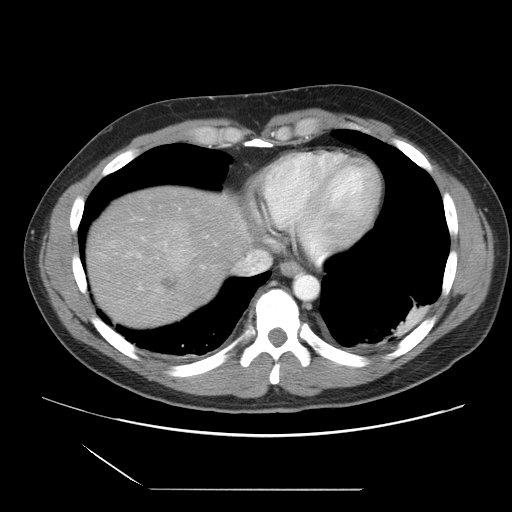
Contrast-enhanced abdominal CT, one axial slice; slice 30 of 39 in the series (ordered by position); 120 kVp; intravenous contrast given; soft-tissue window (W 400 / L 40 HU); 5 mm slice thickness; 512 × 512 image matrix, field of view 395 × 395 mm. Male patient, age 39 years. Case-level facts recorded for this patient, not image findings: diagnosis: colorectal cancer liver metastases, imaged before liver resection; multiple liver metastases: yes; largest metastasis: 1.3 cm; disease in both lobes: no.
Outlined on this slice (expert manual segmentation):
- hepatic veins: box from (x=234, y=252) to (x=257, y=274) px
- liver: (x=86, y=185)–(x=252, y=330)
- planned liver remnant (the part of the liver to remain after resection): (x=149, y=184)–(x=252, y=247)
- portal vein (with intrahepatic branches): (x=125, y=218)–(x=189, y=290)
- liver metastasis: (x=161, y=276)–(x=178, y=292)